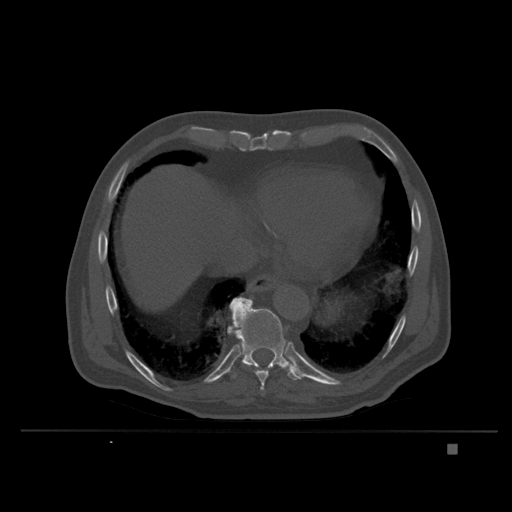
CT including the spine, one axial slice; slice 202 of 435 in the series (ordered by position); bone window (W 1800 / L 400 HU); 1.5 mm slice thickness; 512 × 512 image matrix. Male patient, age 73 years. From the clinical record (not read from this slice): primary cancer: skin.
Structures marked on this image (semi-automatically segmented with operator editing):
- T10 vertebra: box from (x=230, y=299) to (x=302, y=380) px
- T9 vertebra: (x=228, y=297)–(x=272, y=395)